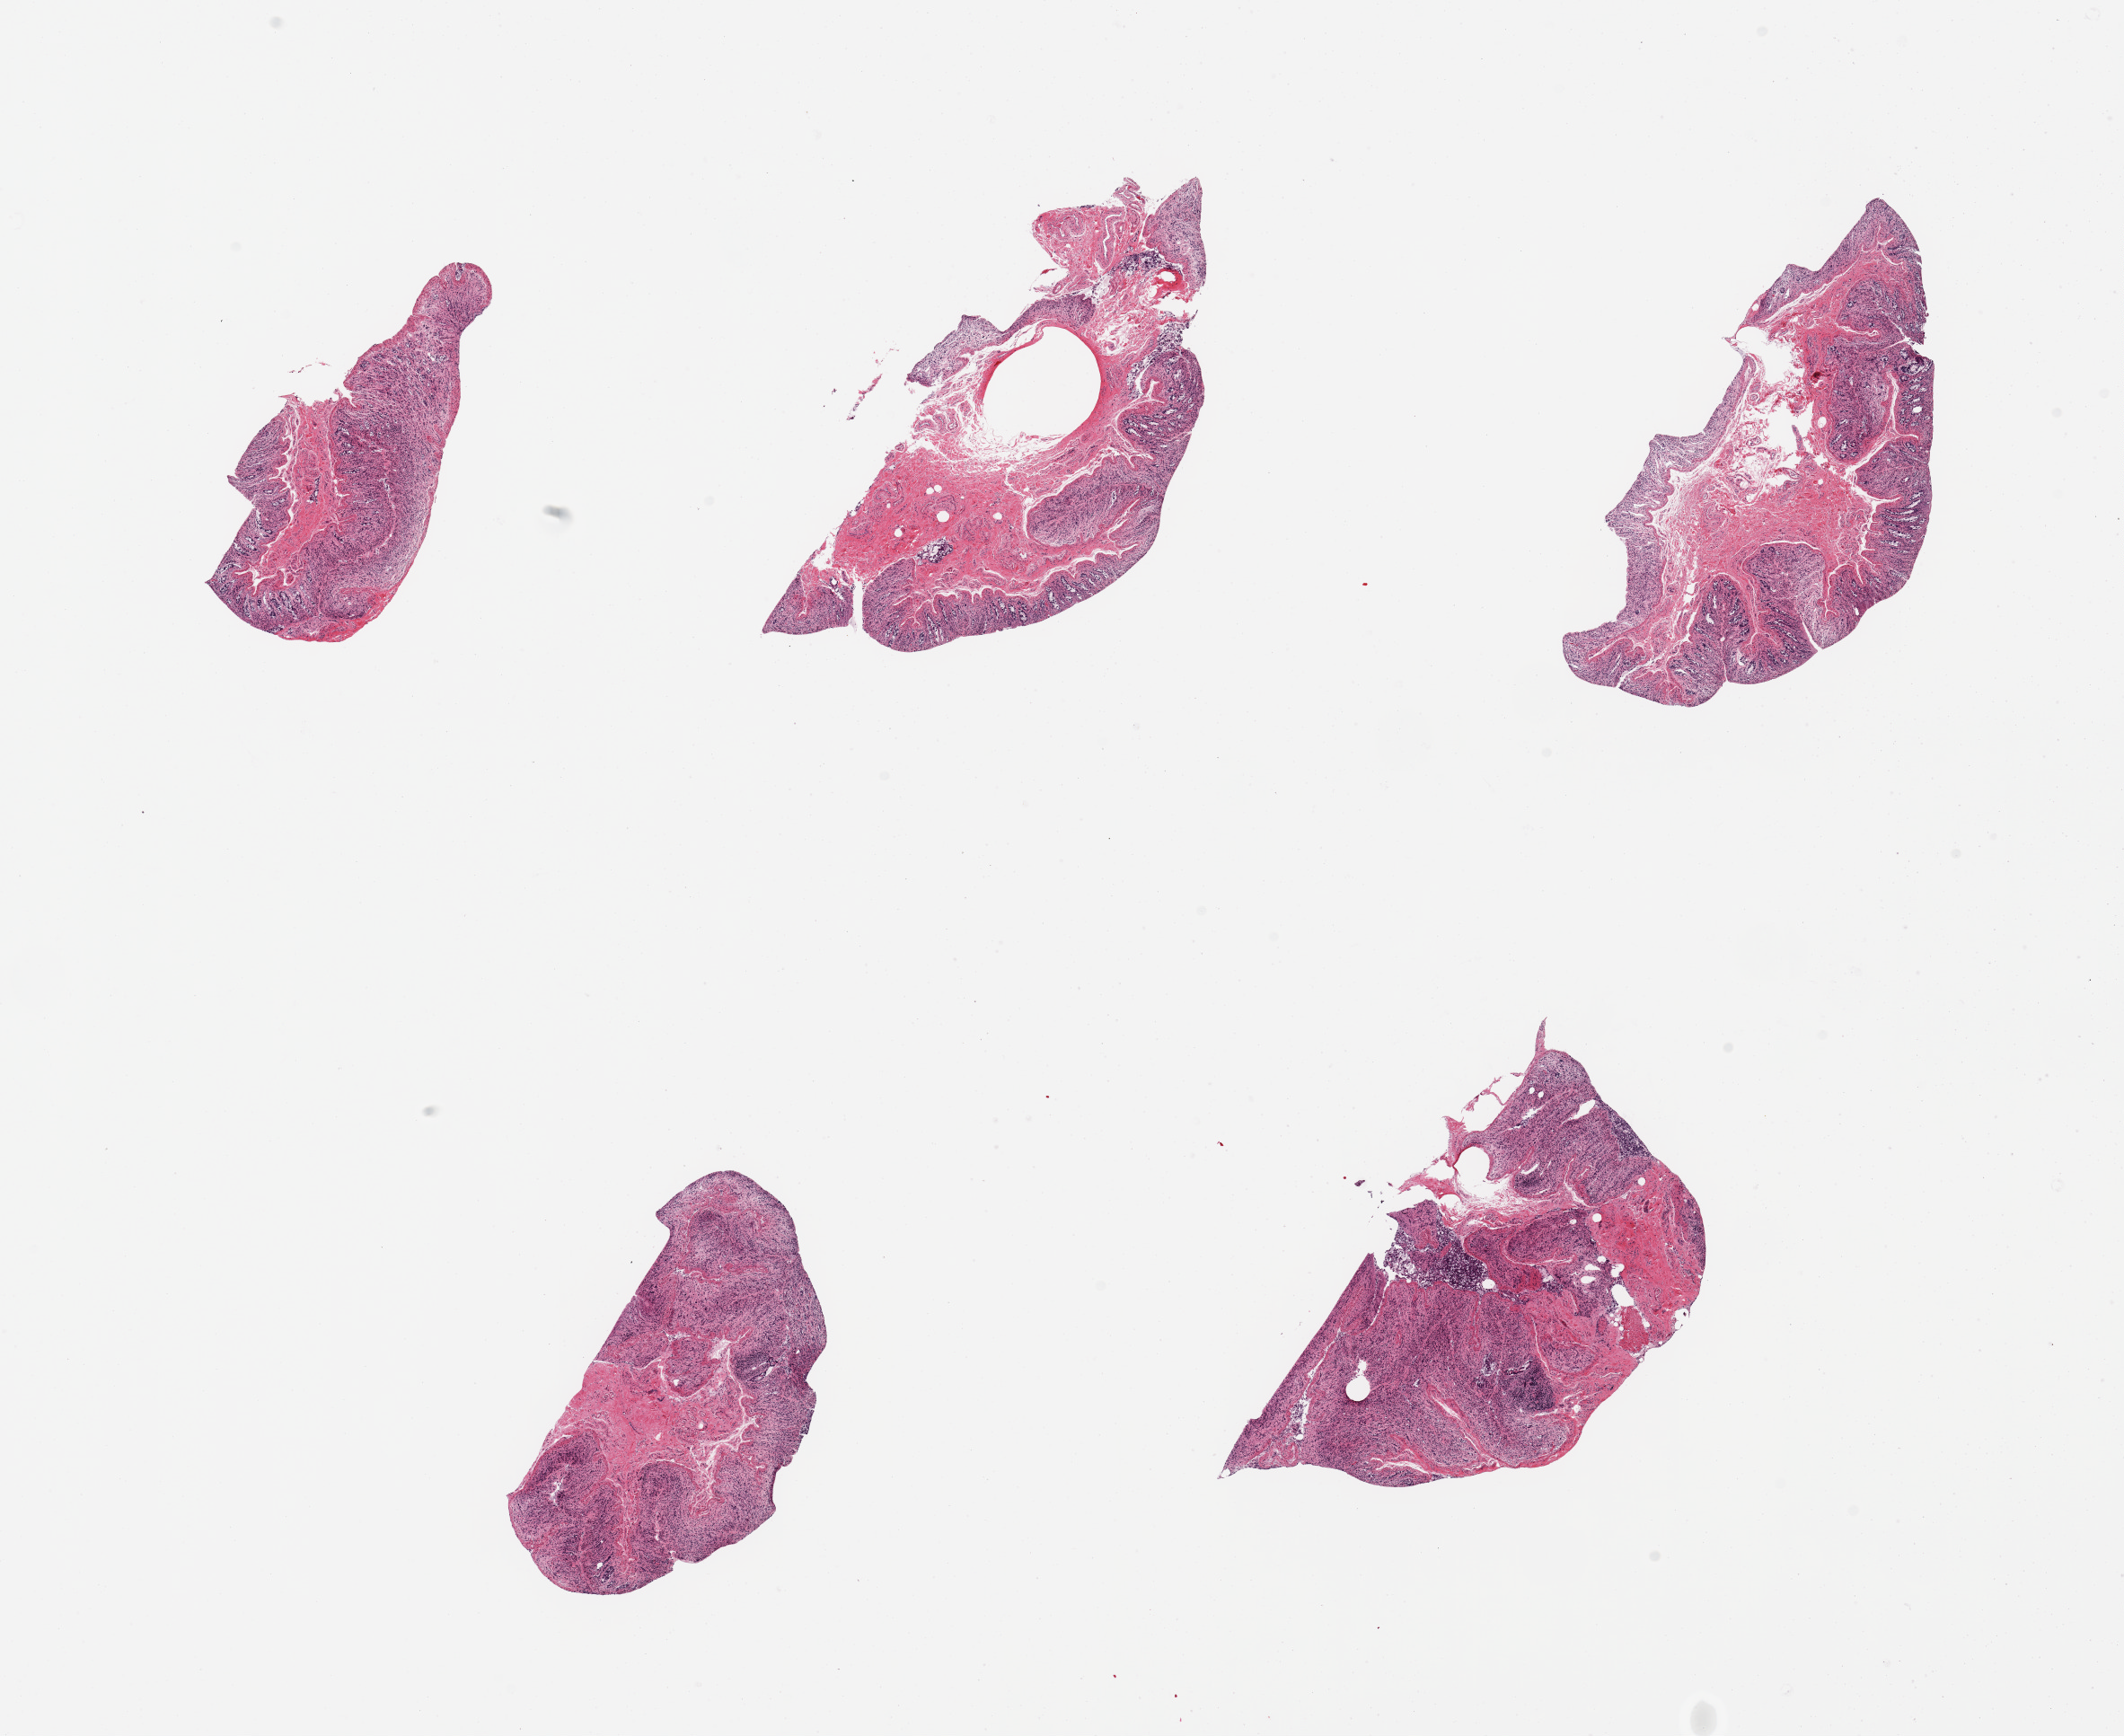
Whole-slide image, hematoxylin and eosin (H&E) stain, shown as a low-resolution overview of the whole scanned area (about 18.7 x 15.3 mm); PAXgene-fixed paraffin-embedded (PFPE) section; target tissue: ileum; donor tissue sample.
Reviewer comment on this tissue sample: 5 pieces, advanced autolysis, insufficient lymphoid aggregates to warrant analysis.